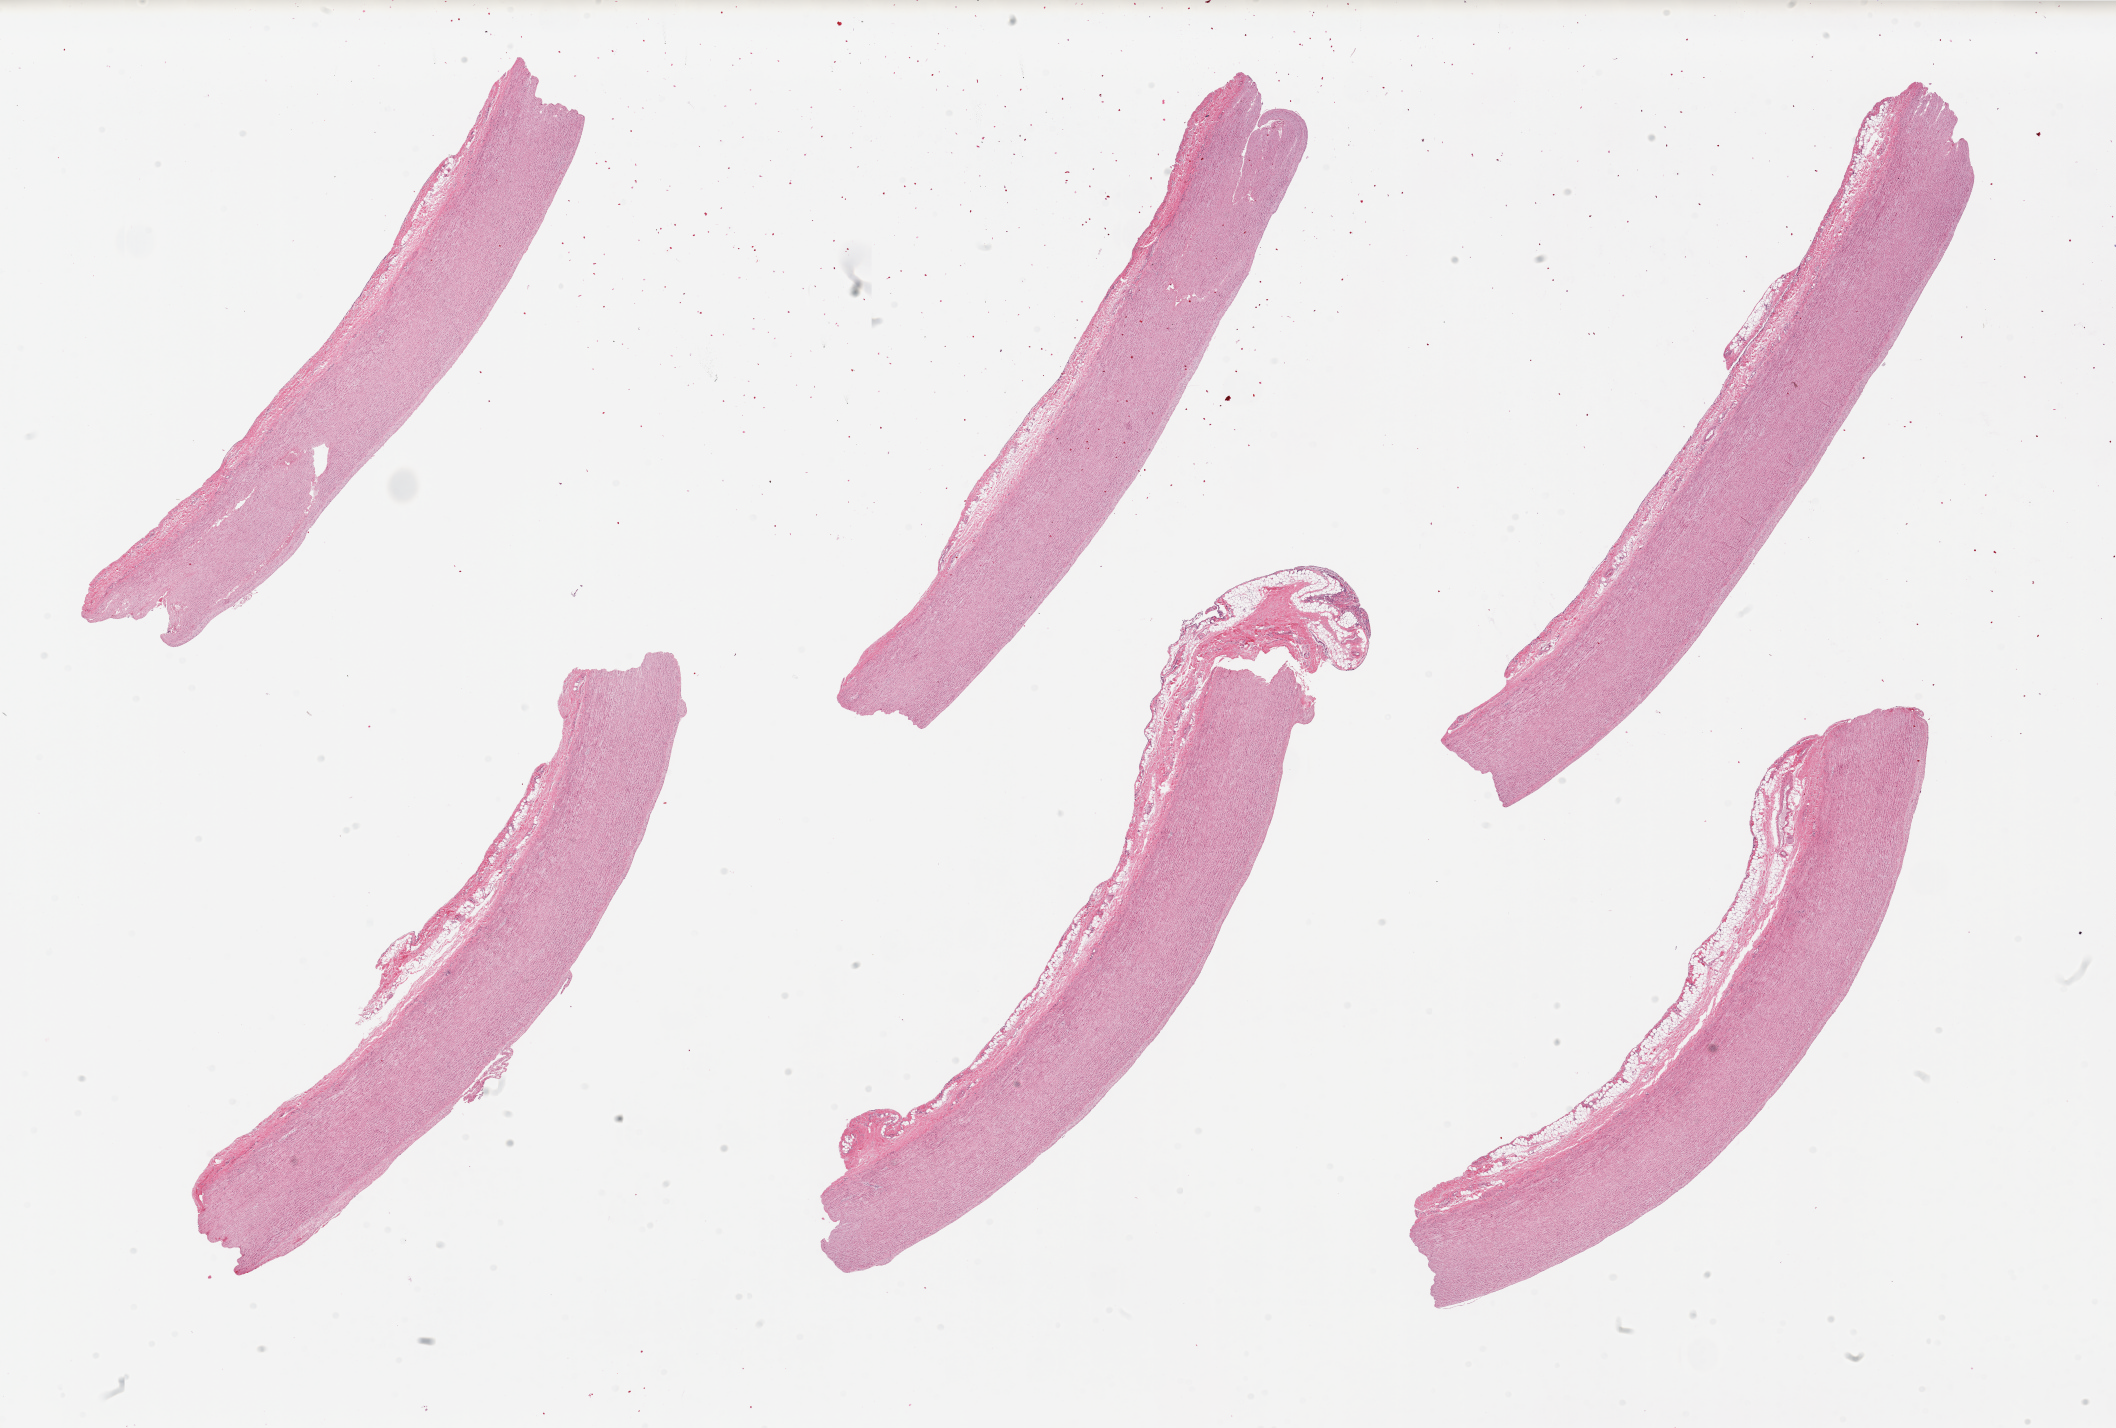
Whole-slide image, haematoxylin and eosin stain, whole scanned area (about 33.5 x 22.6 mm) shown as a low-resolution overview, PAXgene-fixed, paraffin-embedded tissue, section of aorta (target tissue), tissue donor sample. Donor: male.
Reviewer comment on this tissue sample: 6 pieces, fibrofatty adventitia on all pieces.